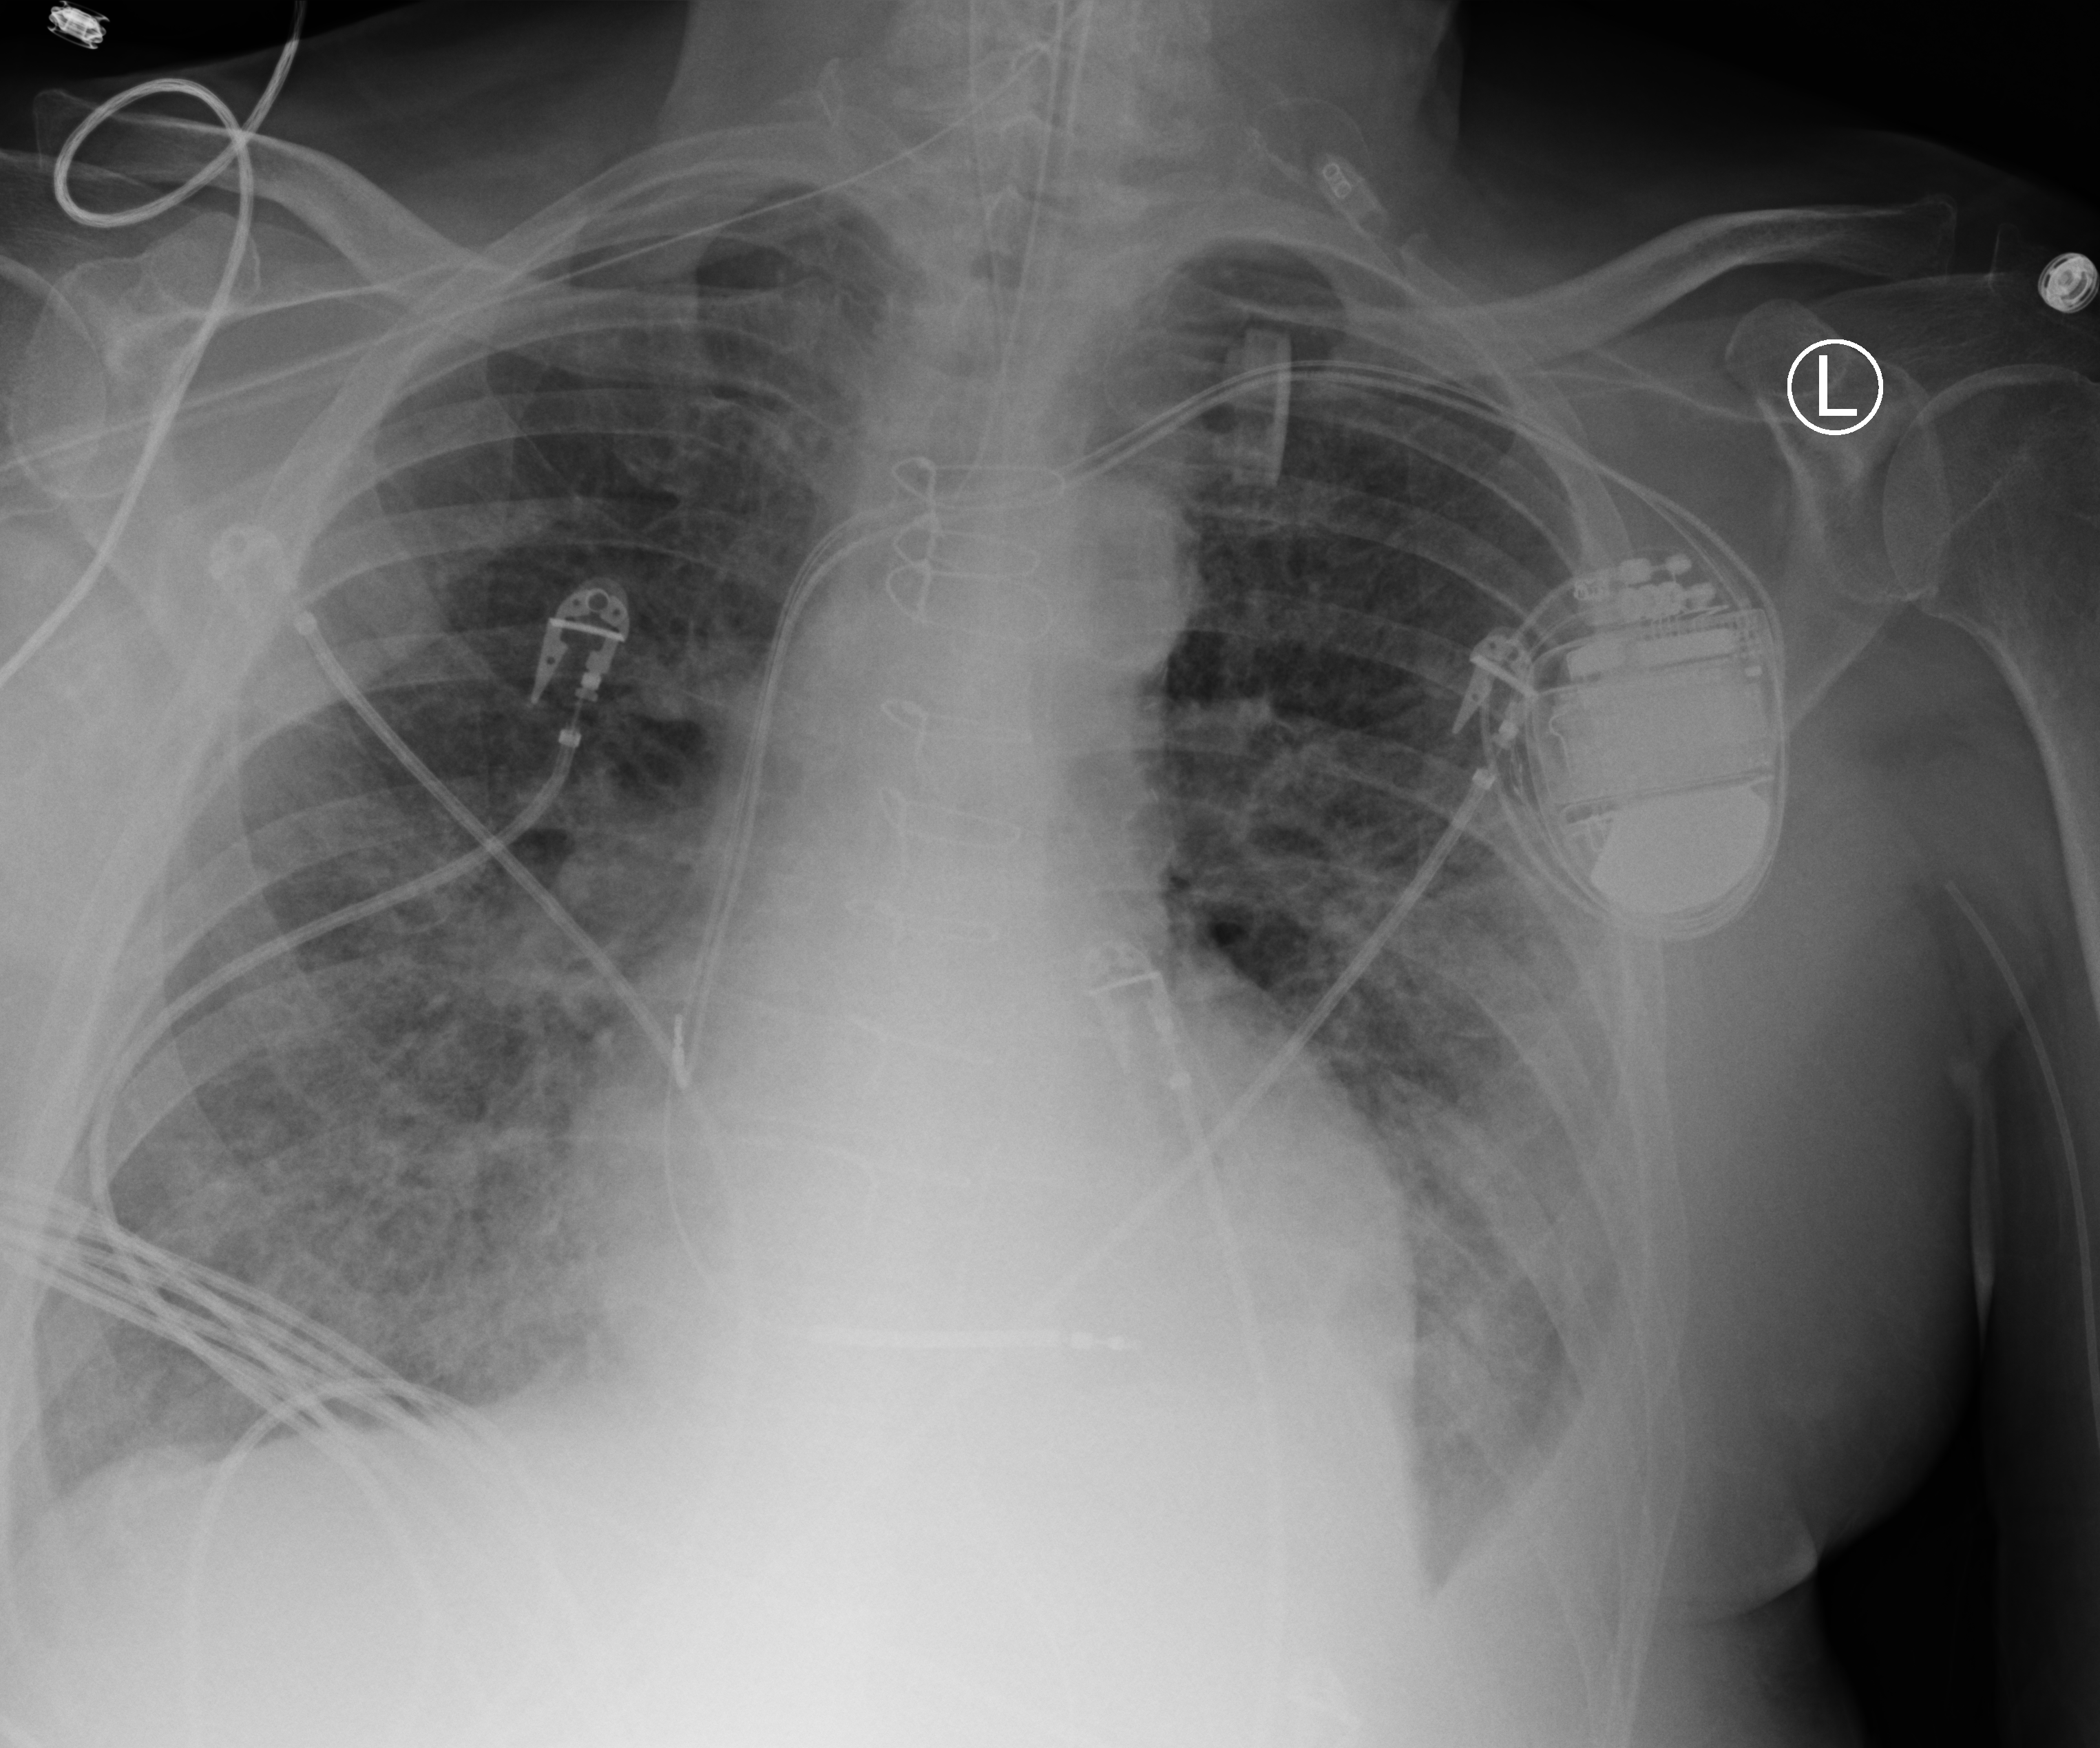
Chest X-ray (portable), anteroposterior (AP) projection. Patient hospitalised with COVID-19; male, aged 75–90 years.
Hospital-stay facts (about this admission, not read from this image; timing relative to this image not recorded): mechanically ventilated during this hospital stay: yes.